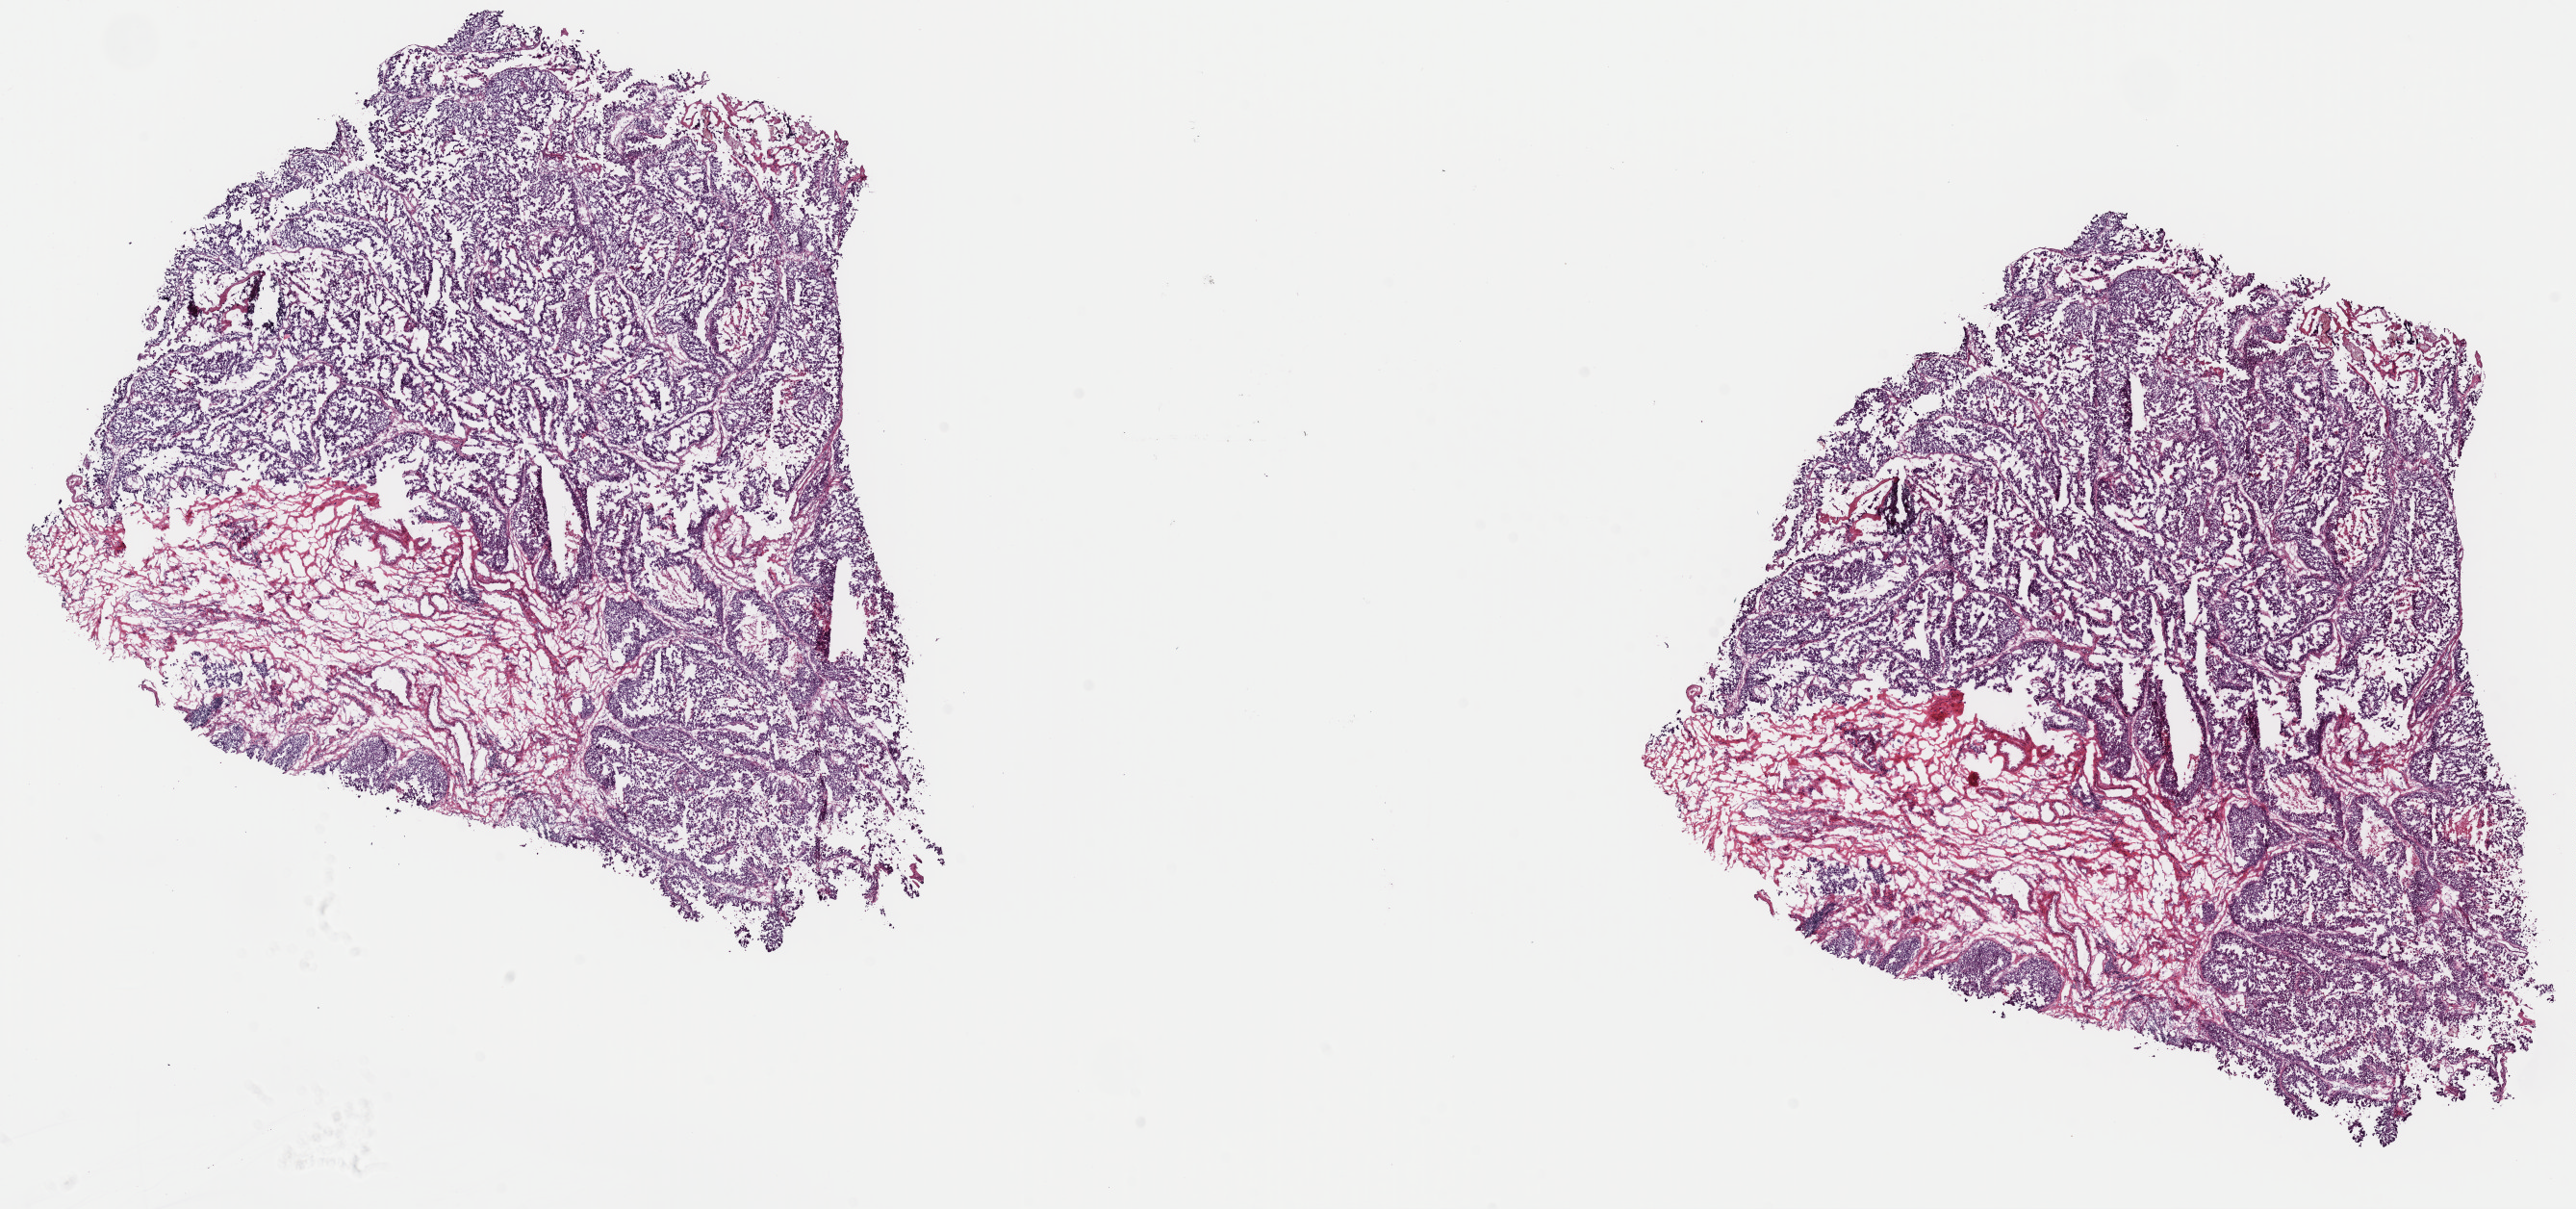
H&E whole-slide image — low-resolution overview of the scanned area, about 21.1 x 9.9 mm (from a 40x scan), frozen section from the top of the tissue portion, sample: primary tumour, bladder. Patient: male, age at initial diagnosis 75 years. Composition of this section per pathologist review: tumour cells 80%, tumour nuclei 90%.
Pathologic diagnosis: Papillary transitional cell carcinoma.